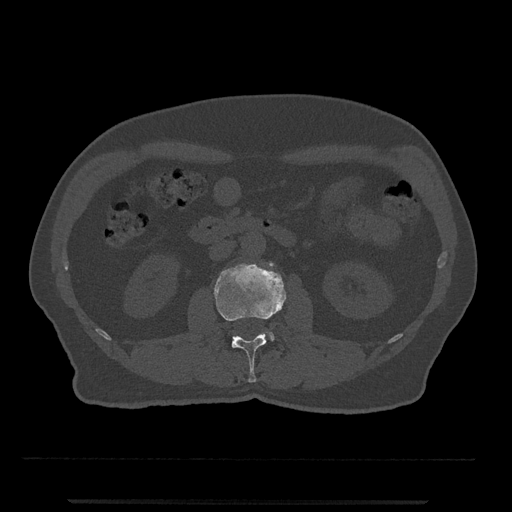
CT including the spine, one axial slice; position 253 of 797 along the scan axis; reconstruction kernel Br40s/3; 120 kVp; bone window (W 1800 / L 400 HU); 512 × 512 image matrix. Patient: male, 63 years. From the clinical record (not read from this slice): primary cancer: prostate.
Structures marked on this image (semi-automatically segmented with operator editing):
- L2 vertebra: bounding box [x1, y1, x2, y2] px = [214, 263, 286, 383]
- L3 vertebra: [269, 332, 275, 341]